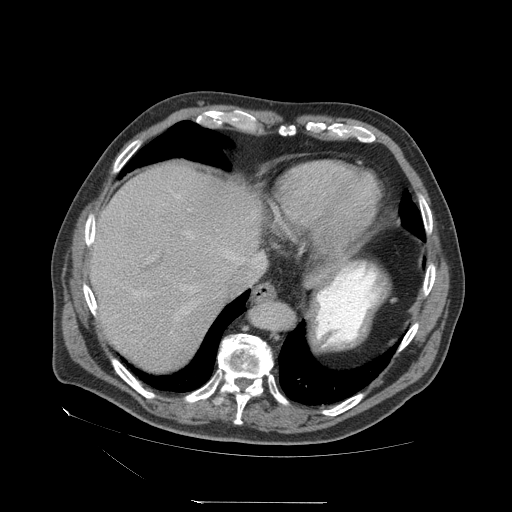
Contrast-enhanced abdominal CT (liver protocol), one axial slice. Position 58 of 83 along the scan axis. Reconstruction kernel STANDARD. Soft-tissue window (W 400 / L 40 HU). 2.5 mm slice thickness. 512 × 512 image matrix, field of view 460 × 460 mm. From the clinical record (not read from this slice): diagnosis: hepatocellular carcinoma (patient treated with transarterial chemoembolisation; whether this scan precedes or follows treatment is not stated here); TNM stage (as recorded): Stage-I; Child-Pugh class: A; tumour differentiation: well differentiated; tumour nodularity: uninodular.
Annotated regions visible in this slice (semi-automatically segmented with operator editing):
- abdominal aorta: bounding box [x1, y1, x2, y2] px = [254, 302, 295, 331]
- liver parenchyma outside the tumour (the mass and vessels are separate outlines, so this box may not span the whole liver): [90, 164, 262, 372]
- liver vessels: [134, 196, 228, 314]